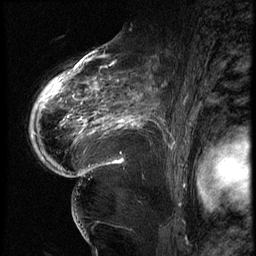
Breast MRI (dynamic contrast-enhanced), one sagittal slice; position 43 of 62 along the scan axis; 3 images stored at this slice position (order not interpretable as contrast timing); 1.5 T; TE 4.2 ms, TR 9 ms; 256 × 256 image matrix, field of view 180 × 180 mm. Female patient, age 56 years. Case-level facts recorded for this patient, not image findings: setting: breast cancer imaged before/during neoadjuvant chemotherapy; receptor status: HER2-positive.
Structures marked on this image (semi-automatically segmented with operator editing):
- analysis volume of interest (the breast-tissue region the enhancement analysis was run in; not a lesion): bounding box [x1, y1, x2, y2] px = [84, 75, 181, 153]
- tumour enhancement mask (voxels above the 140 % enhancement threshold inside the analysis volume of interest): [84, 77, 162, 137]